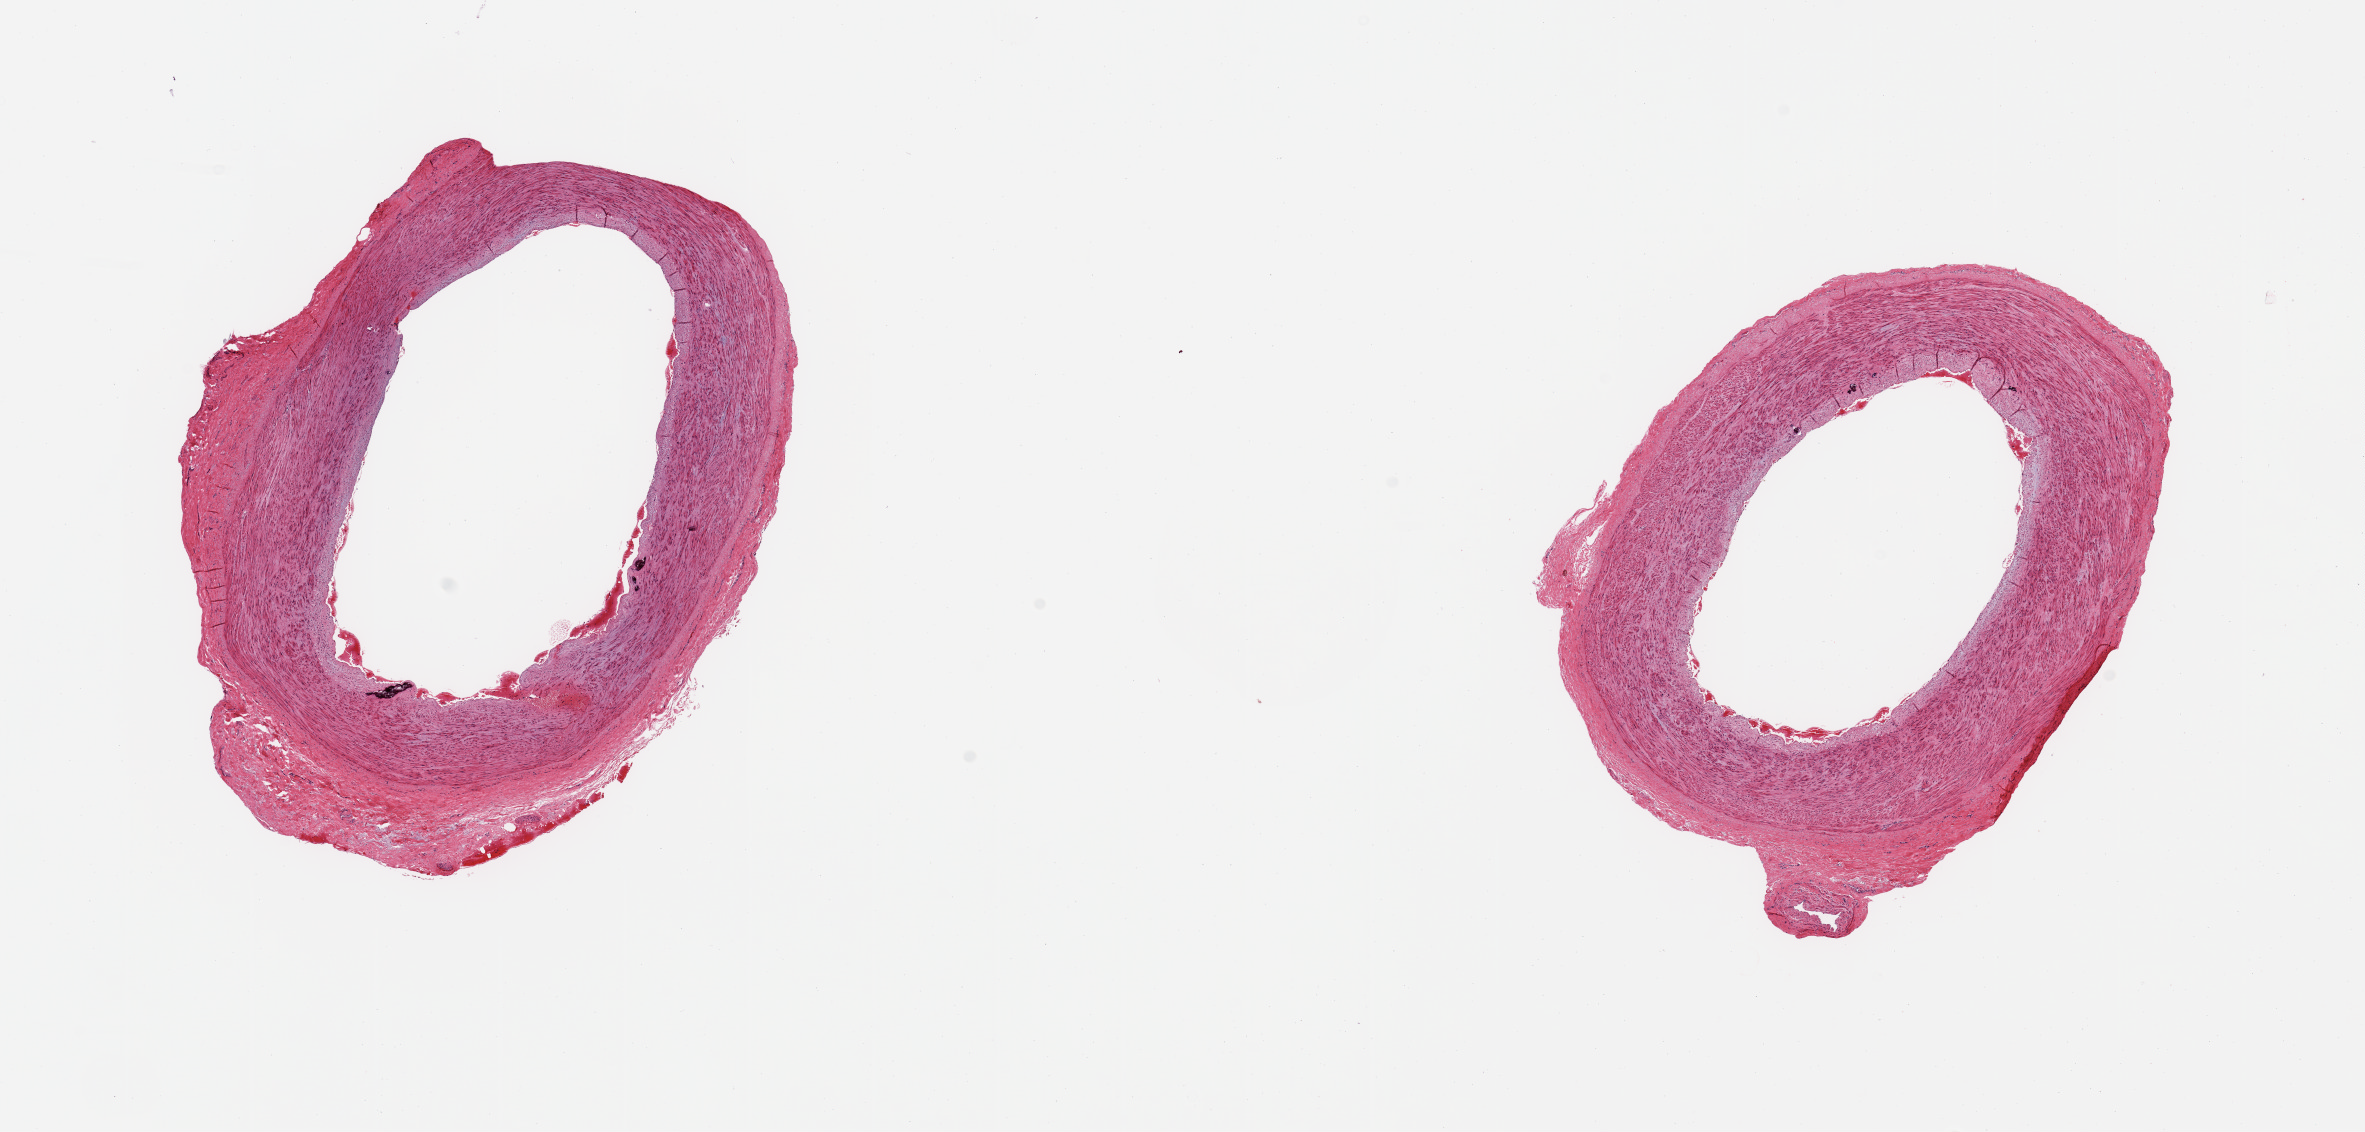
Whole-slide image, H&E stain, low-resolution overview of the scanned area, about 18.7 x 9.0 mm (acquisition: 20x scan); PAXgene-fixed, paraffin-embedded tissue; target tissue: tibial artery; tissue donor sample. Donor sex: male.
Review note (as recorded): 2 pieces; some intimal thickening, focal calcifications.